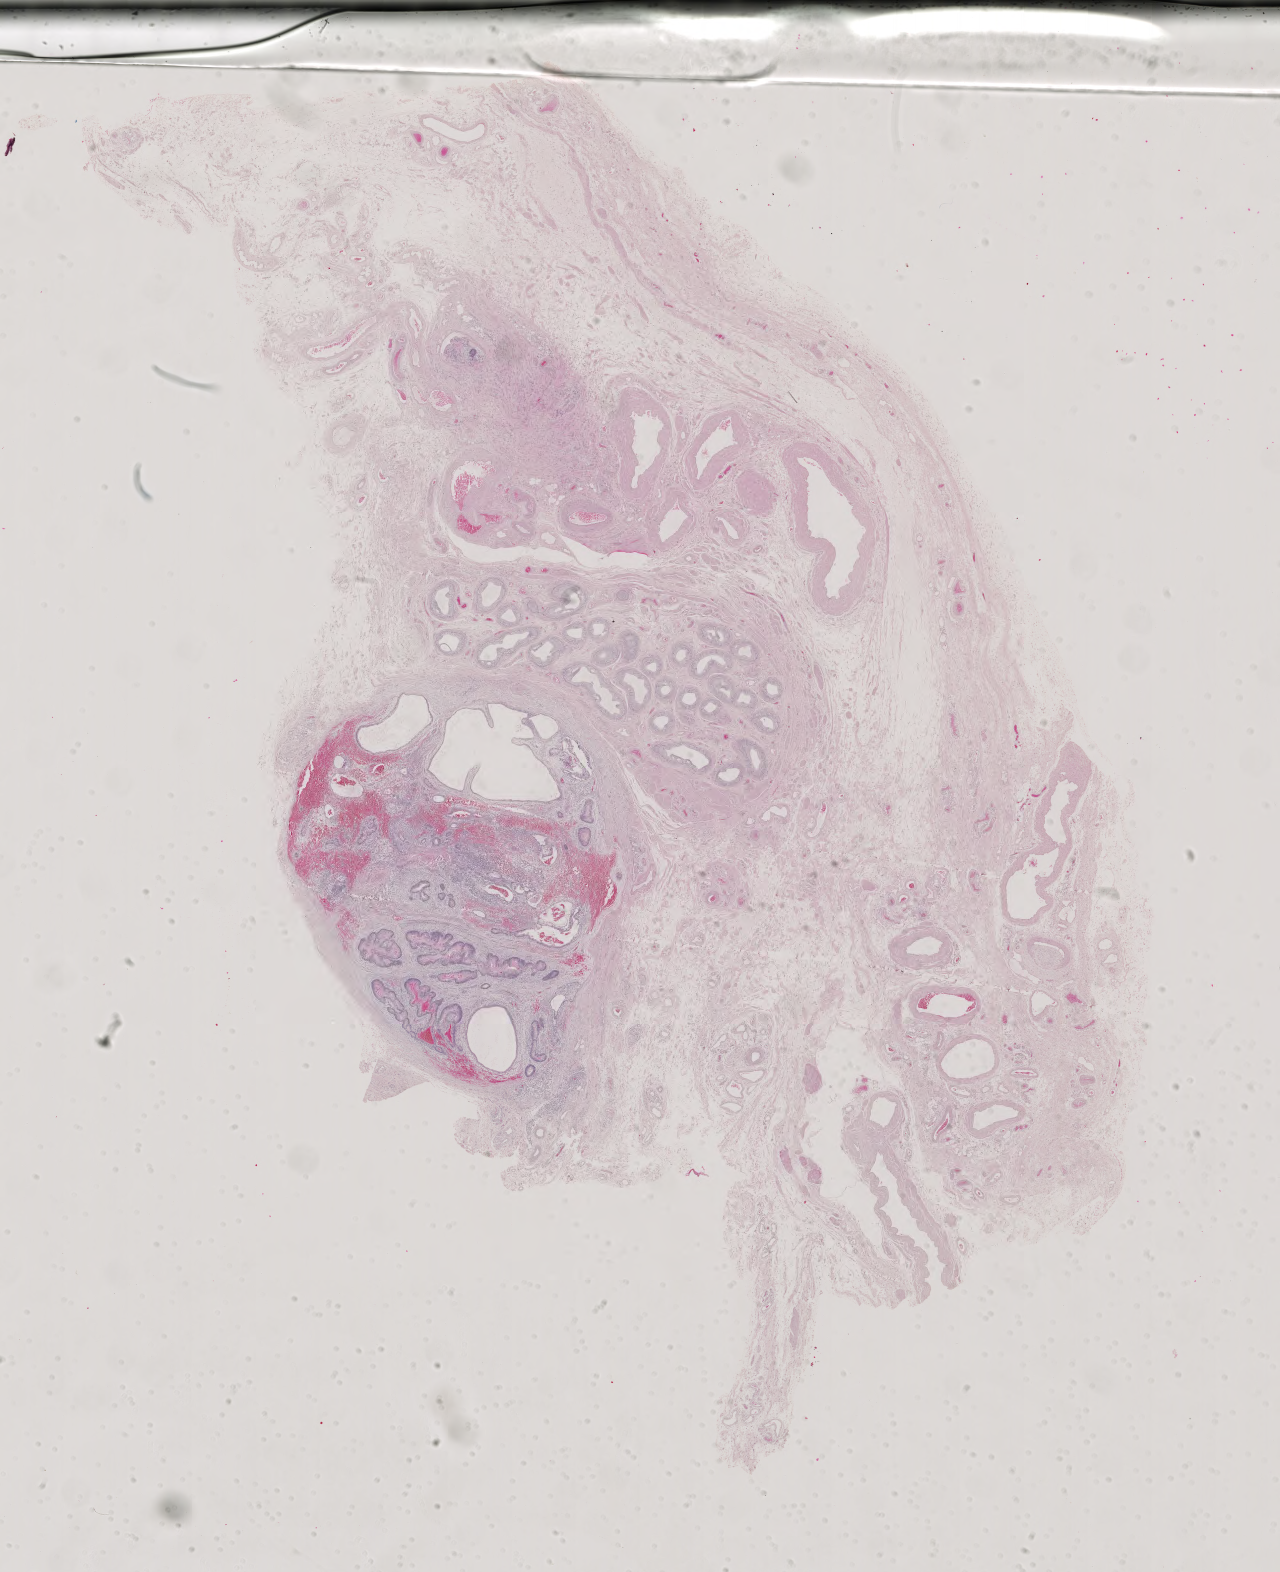
H&E-stained whole-slide image — low-resolution overview of the scanned area, about 18.7 x 22.9 mm; formalin-fixed paraffin-embedded (FFPE) diagnostic section; testis, primary tumour sample. Male, age 20 years at initial diagnosis.
Laterality: left. Histologic diagnosis: Mixed germ cell tumor. AJCC pathologic stage: IIIC (6th edition).